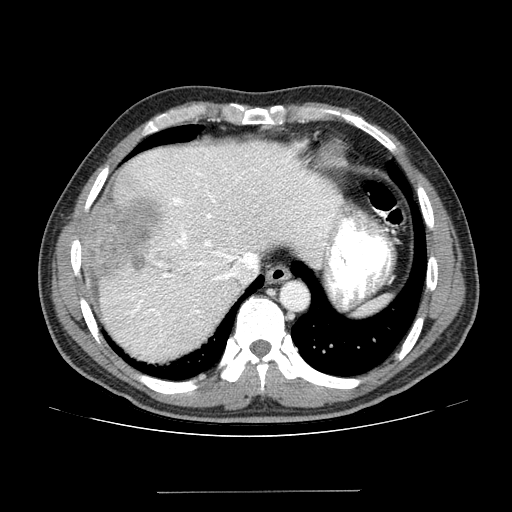
Contrast-enhanced abdominal CT (liver protocol), one axial slice. Slice 110 of 131 in the series (ordered by position). Reconstruction kernel STANDARD. 100 kVp. One of 2 acquisitions stored at this slice position. Soft-tissue window (W 400 / L 40 HU). 2.5 mm slice thickness. 512 × 512 image matrix, field of view 380 × 380 mm. Case-level facts recorded for this patient, not image findings: diagnosis: hepatocellular carcinoma (patient treated with transarterial chemoembolisation; whether this scan precedes or follows treatment is not stated here); TNM stage (as recorded): Stage-I; Child-Pugh class: A; tumour differentiation: poorly differentiated; tumour size: 10.3 cm.
Annotated regions visible in this slice (semi-automatically segmented with operator editing):
- abdominal aorta: box from (x=281, y=283) to (x=307, y=309) px
- liver parenchyma outside the tumour (the mass and vessels are separate outlines, so this box may not span the whole liver): (x=82, y=140)–(x=342, y=362)
- mass: (x=84, y=197)–(x=162, y=278)
- liver vessels: (x=121, y=149)–(x=334, y=343)